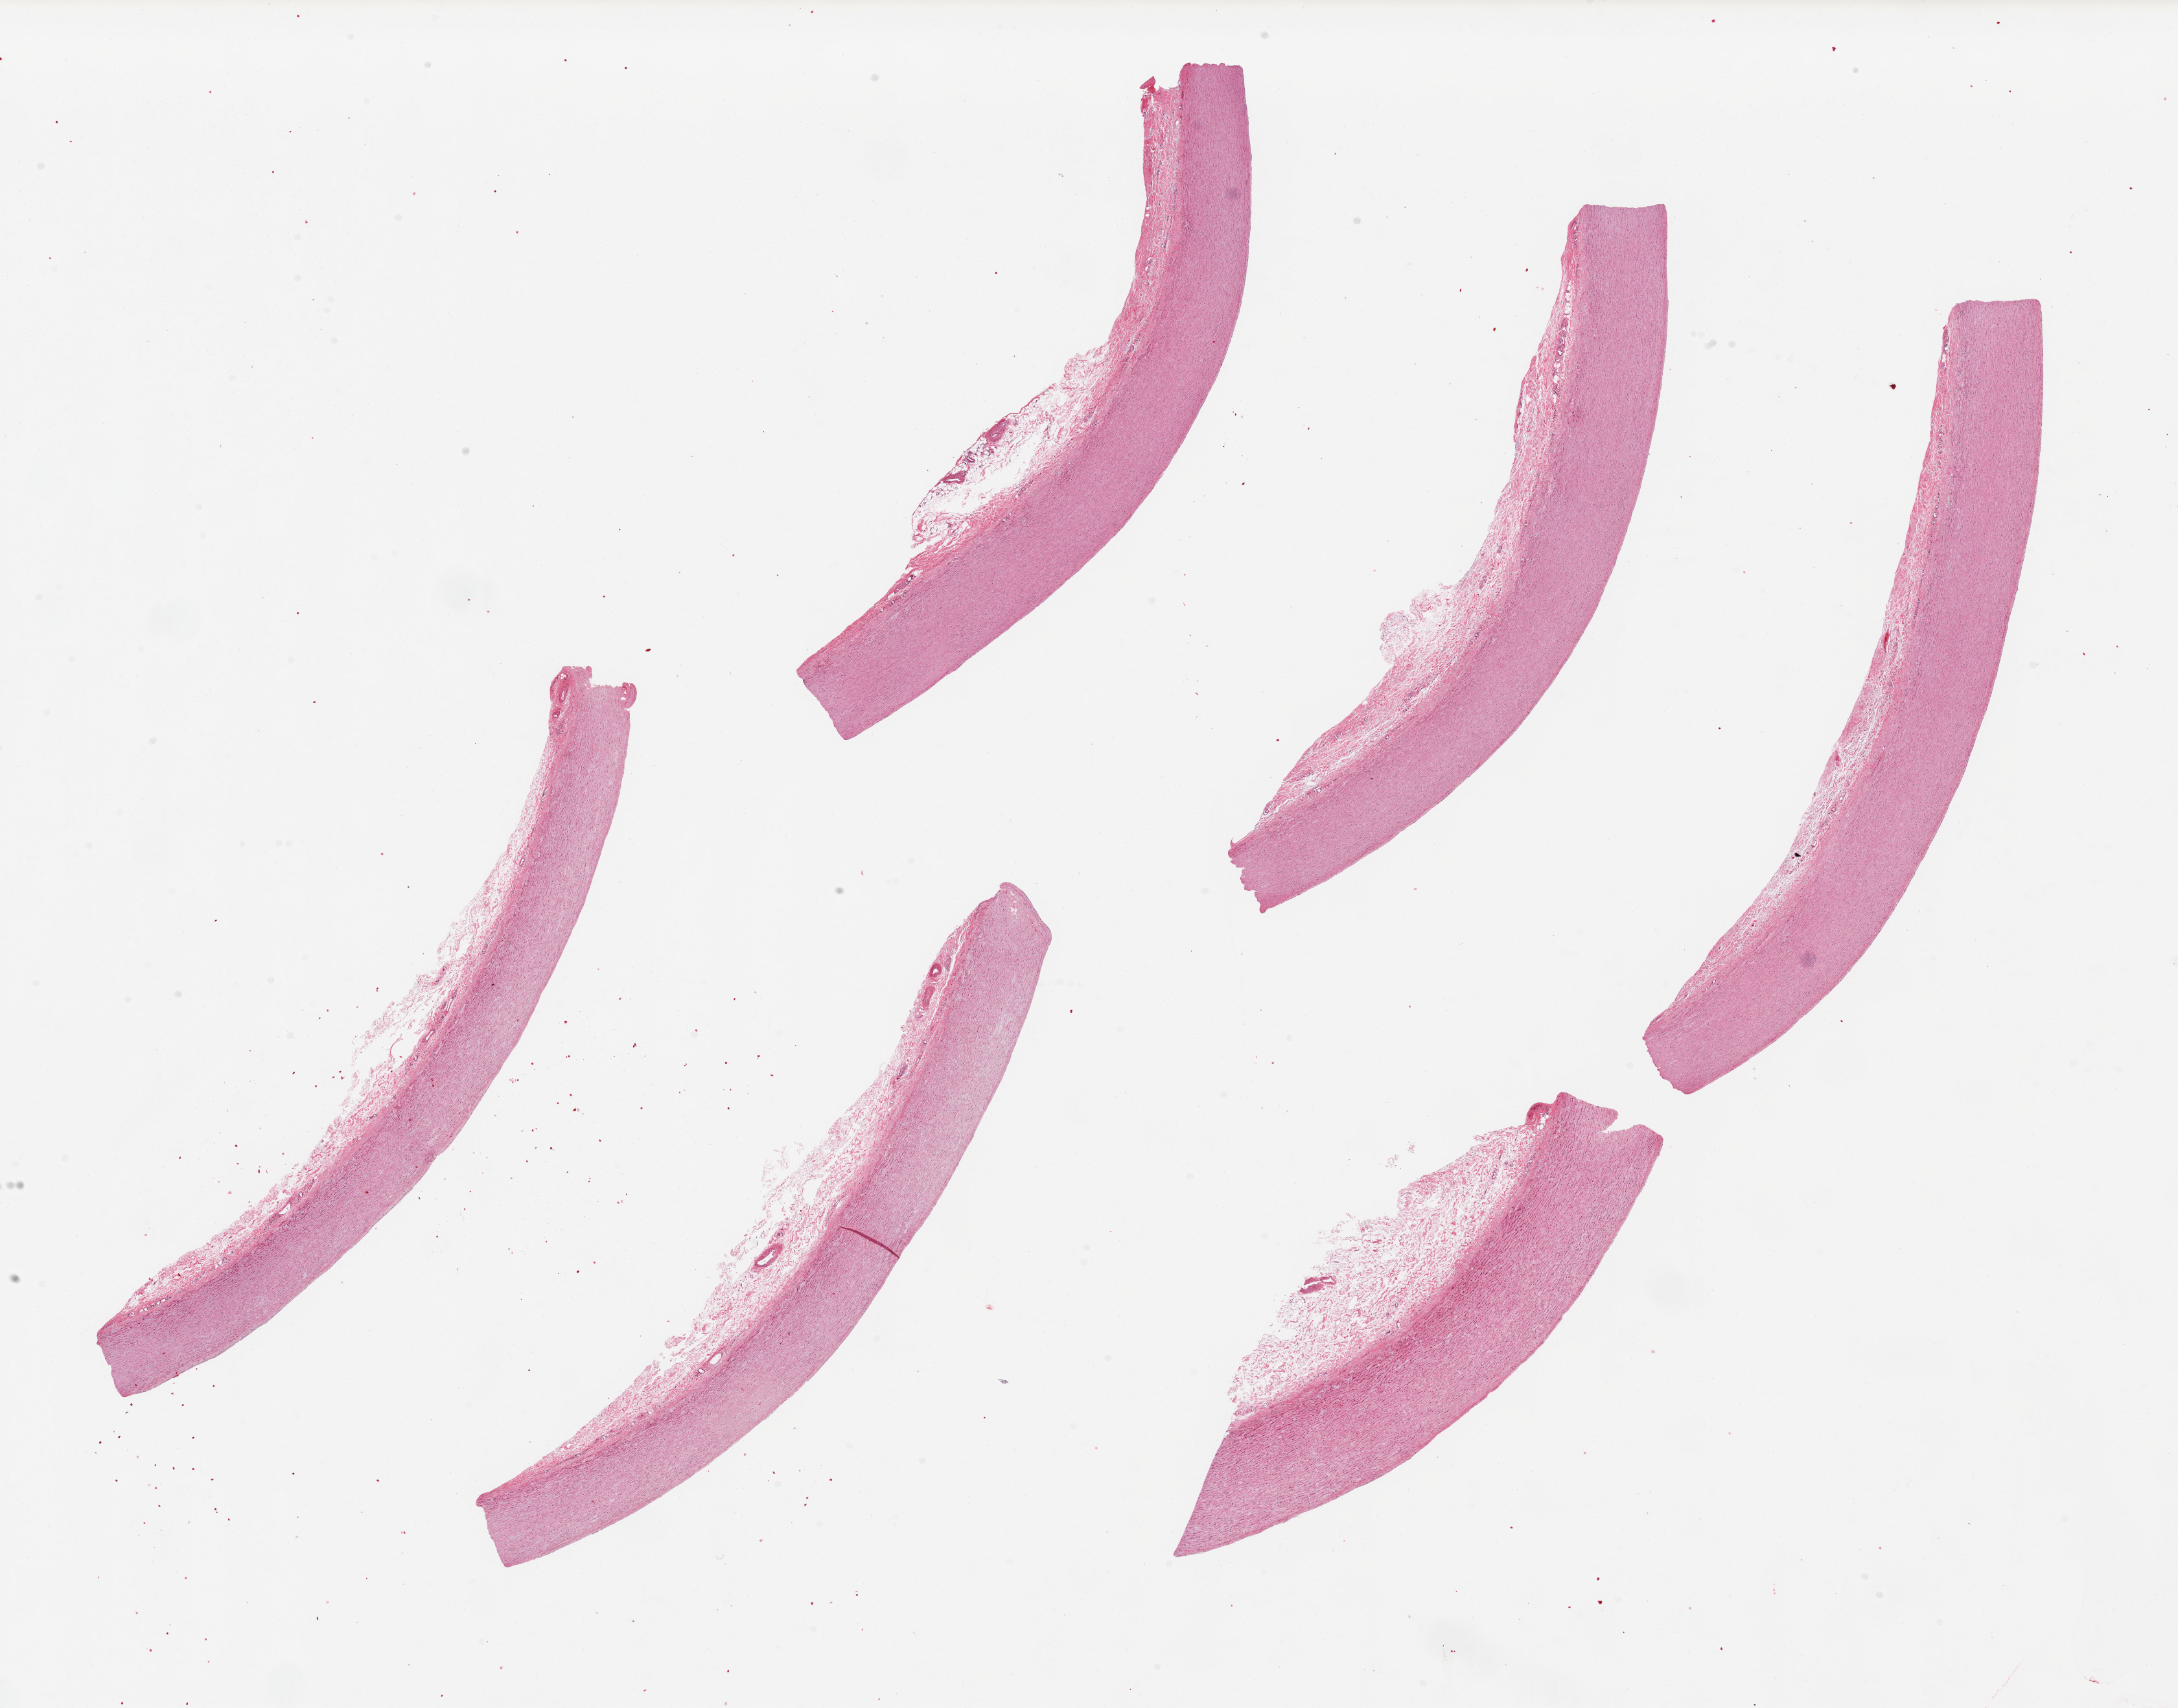
Haematoxylin and eosin whole-slide image, whole scanned area (about 26.6 x 20.8 mm, acquisition: 20x scan) shown as a low-resolution overview. PAXgene-fixed paraffin-embedded (PFPE) section. Target tissue: aorta. Donor tissue sample. Female donor.
Review note (as recorded): 6 pieces up to 10x1.5 mm; no plaques.